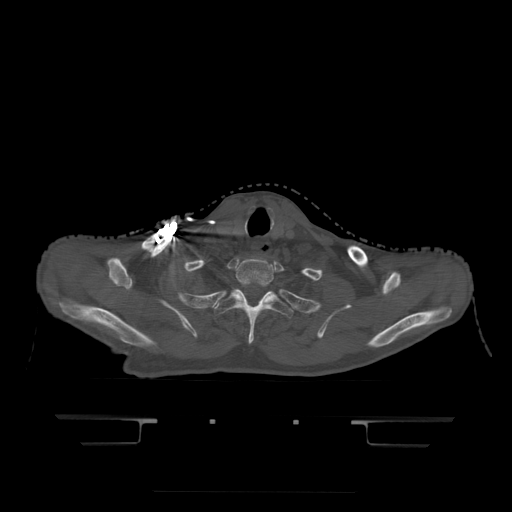
CT including the spine, one axial slice; position 392 of 522 along the scan axis; bone window (W 1800 / L 400 HU); 1.25 mm slice thickness; 512 × 512 image matrix, field of view 436 × 436 mm. Patient age 68 years. Case-level facts recorded for this patient, not image findings: primary cancer: urothelial.
Structures marked on this image (semi-automatically segmented with operator editing):
- T1 vertebra: box from (x=236, y=259) to (x=274, y=288) px
- T2 vertebra: (x=215, y=289)–(x=293, y=345)